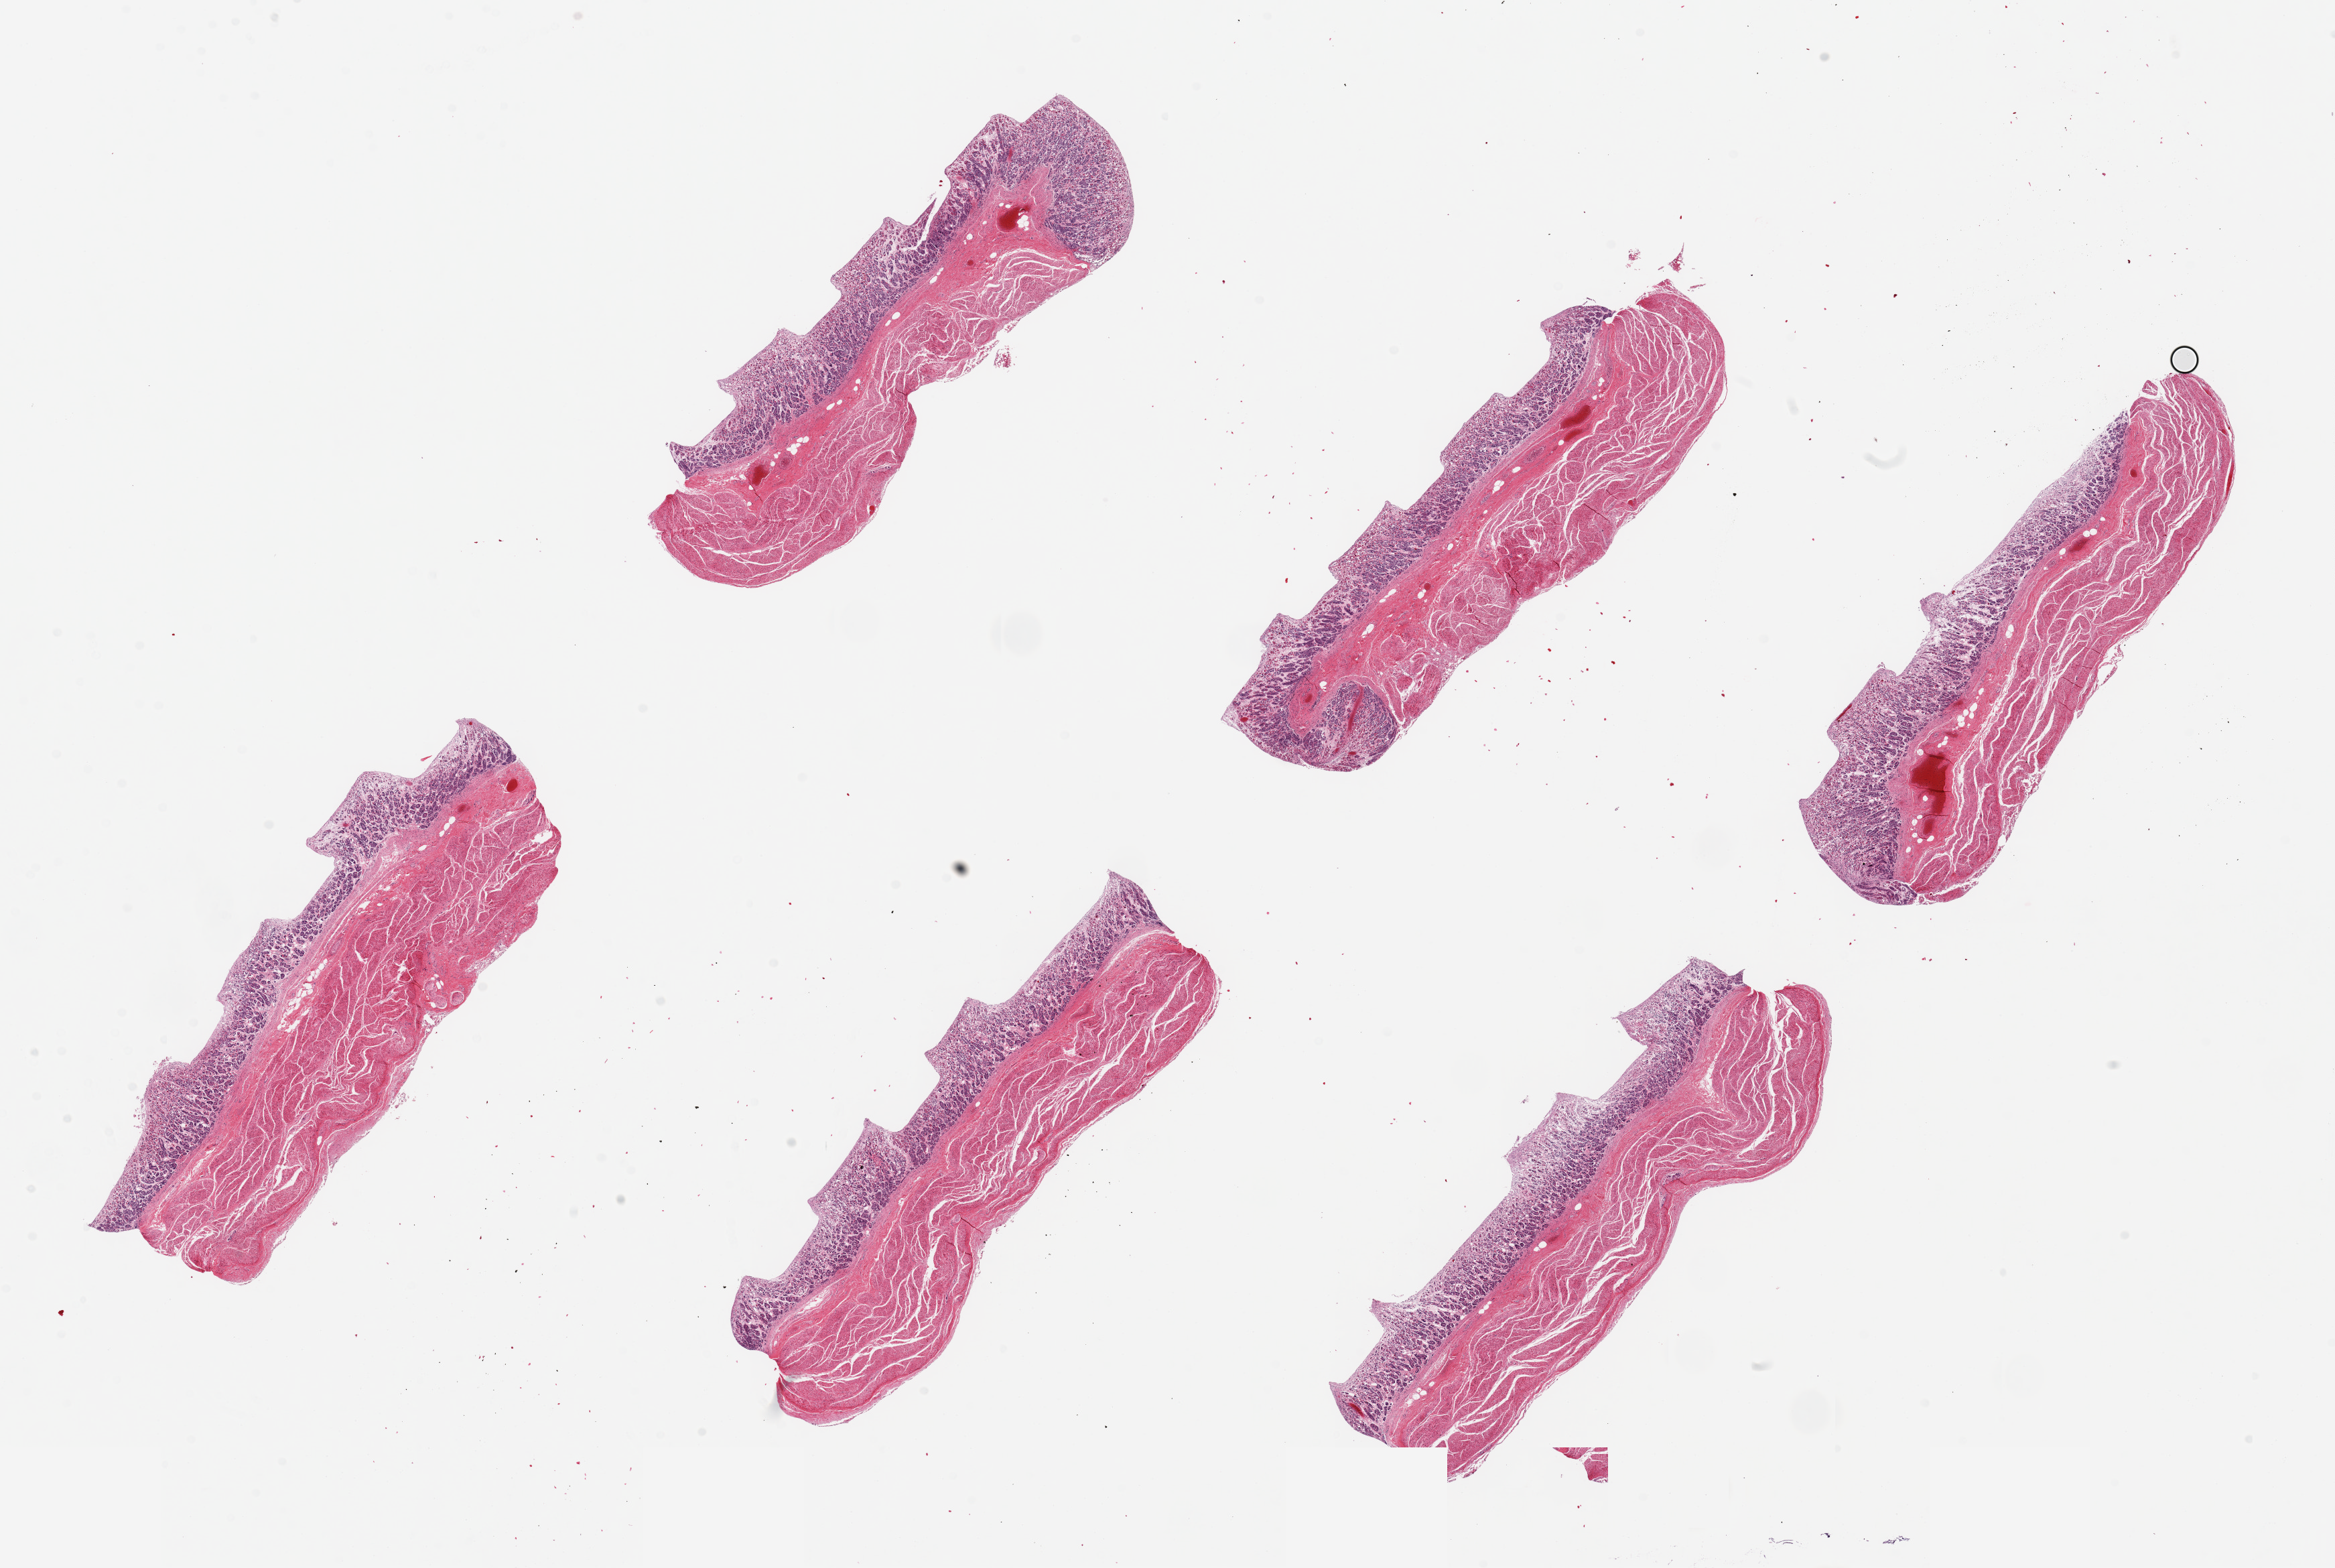
Whole-slide image, haematoxylin and eosin stain, low-resolution overview of the scanned area, about 27.6 x 18.5 mm (acquisition: 20x scan). PAXgene-fixed paraffin-embedded (PFPE) section. Sampled site (target tissue): stomach. Tissue donor sample. Donor sex: male.
- review note (as recorded): 6 pieces, up to 8x2mm; superficial half of oxyntic mucosa is sloughed, deeper in better condition